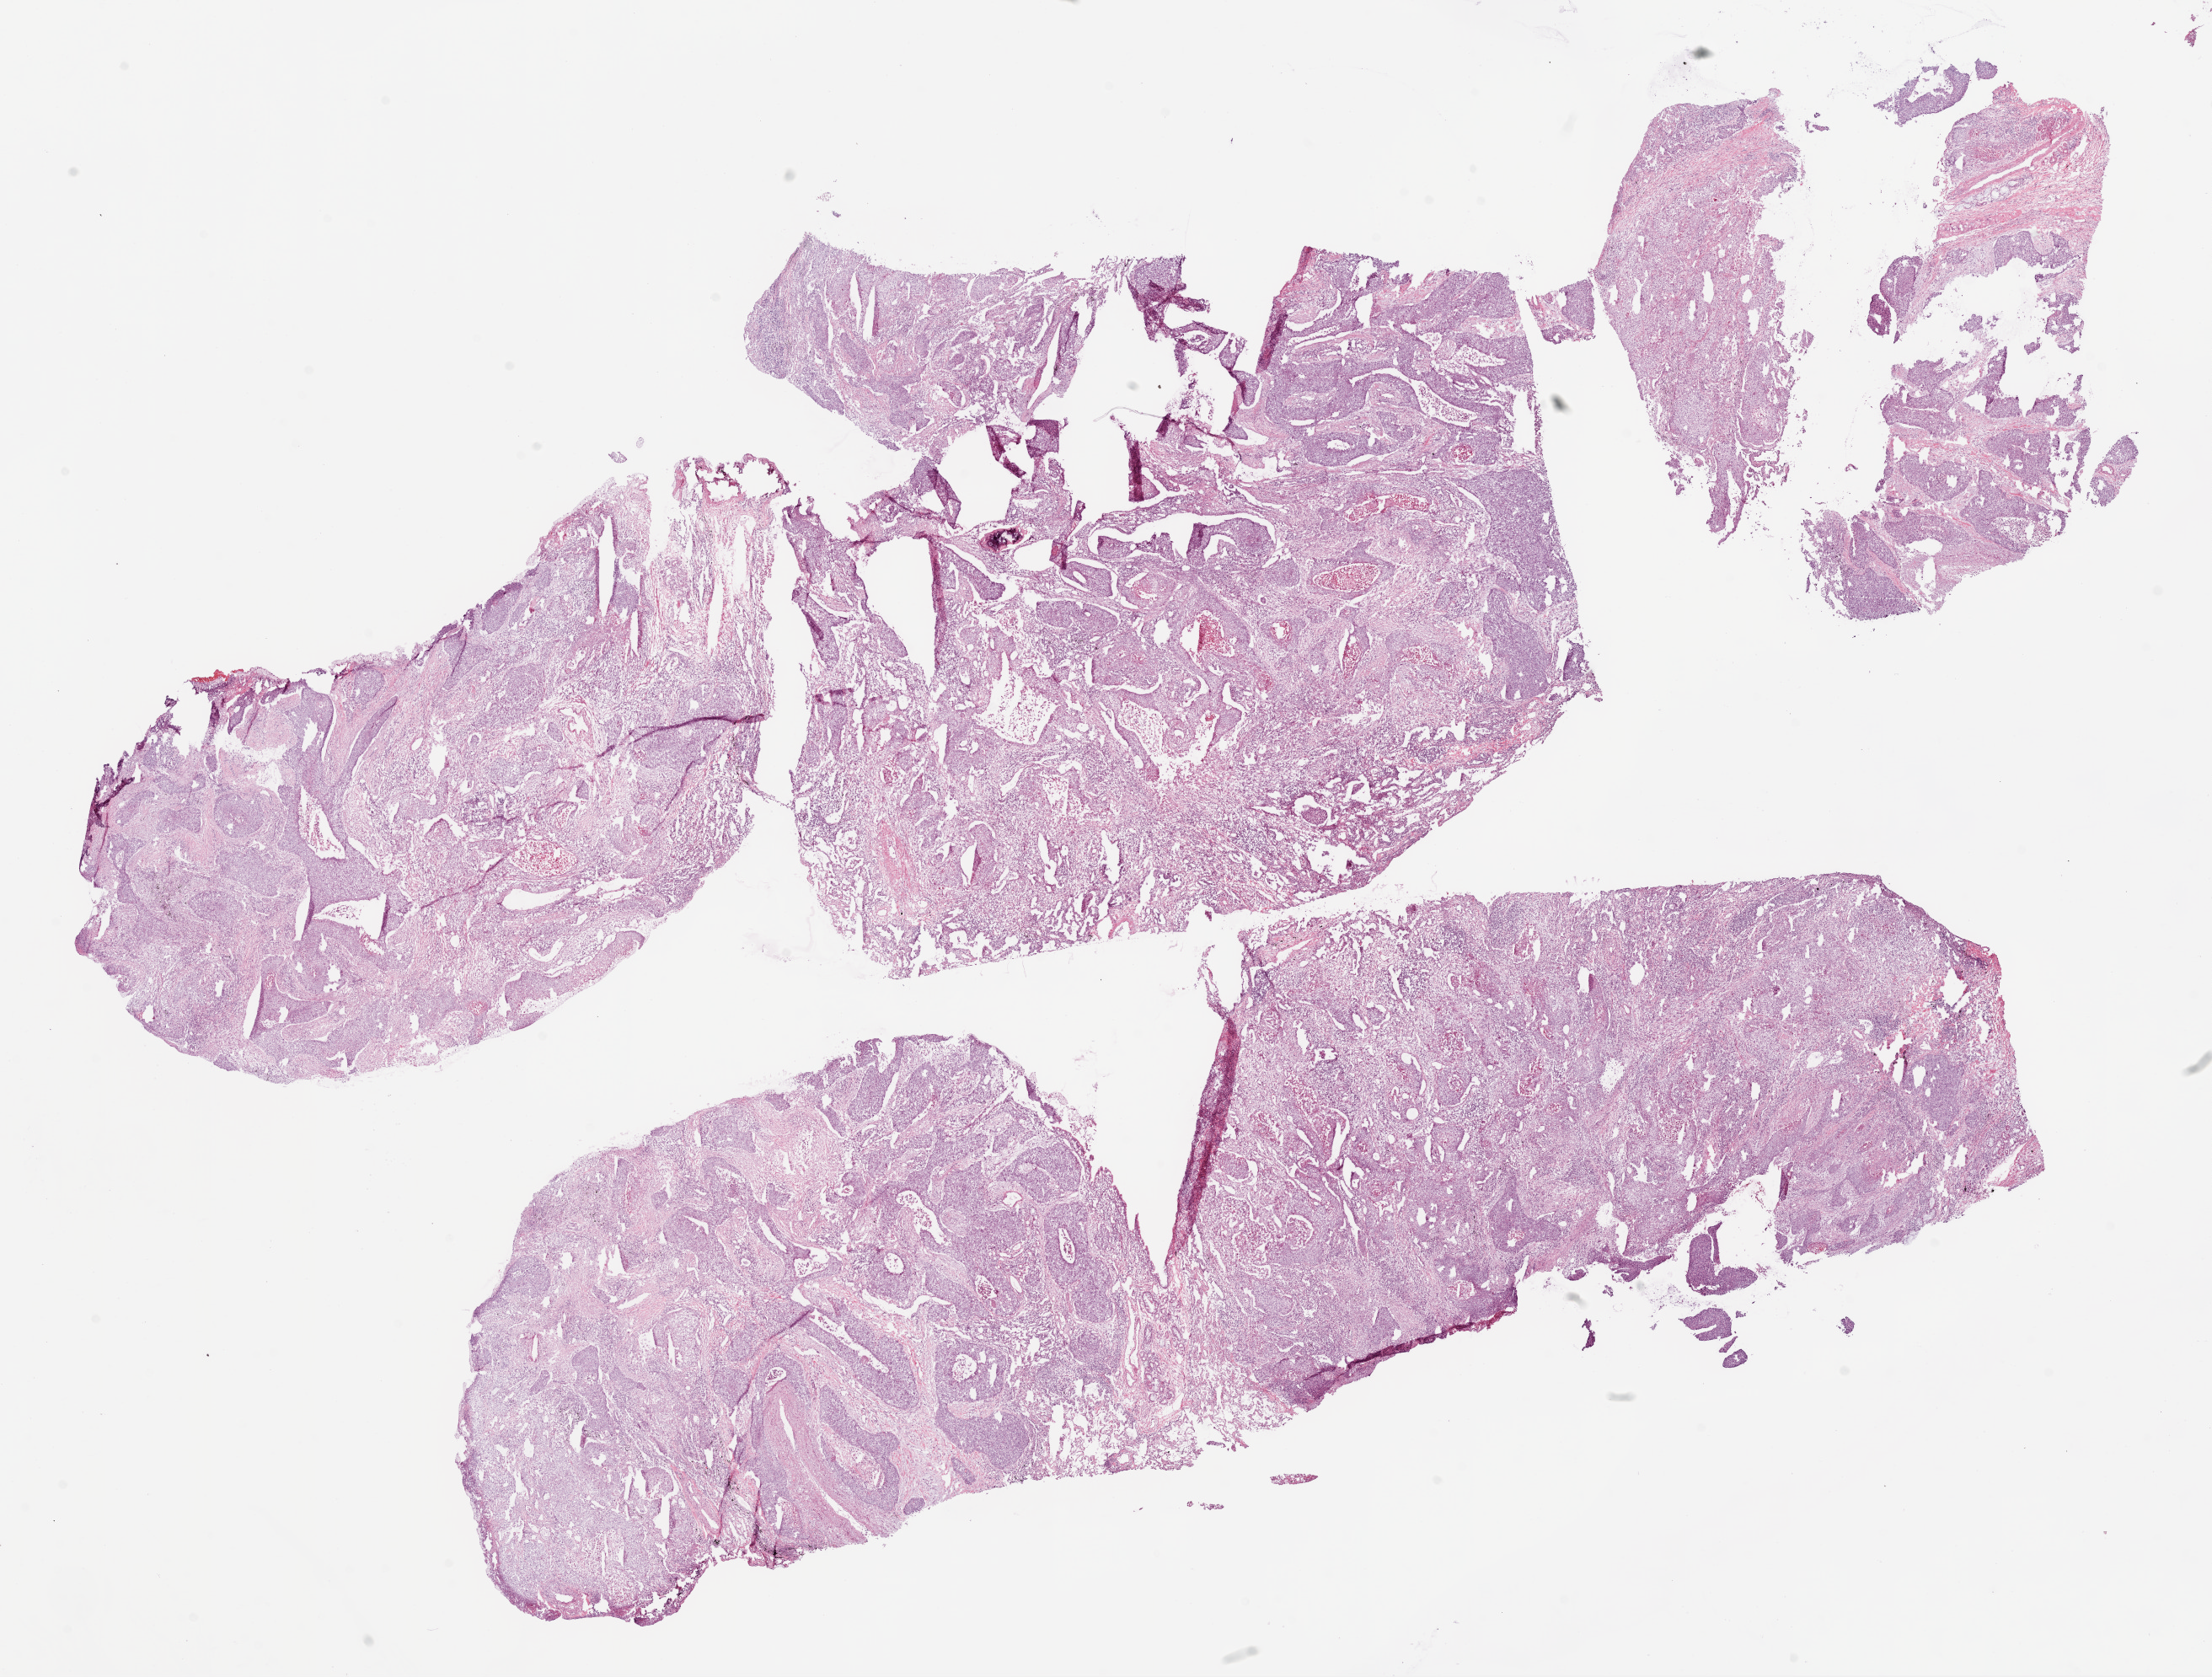
H&E-stained whole-slide image, a low-resolution overview of the entire scanned area, about 21.1 x 16.0 mm, frozen section from the top of the tissue portion, sample: primary tumour, lung. Female patient; age at initial diagnosis 76 years. Pathologist review of this section (percent, as recorded): tumour cells 65%, tumour nuclei 70%, normal cells 5%, stromal cells 20%, necrosis 10%.
Pathologic diagnosis: Squamous cell carcinoma, NOS (upper lobe, lung). AJCC pathologic stage: IA (6th edition).